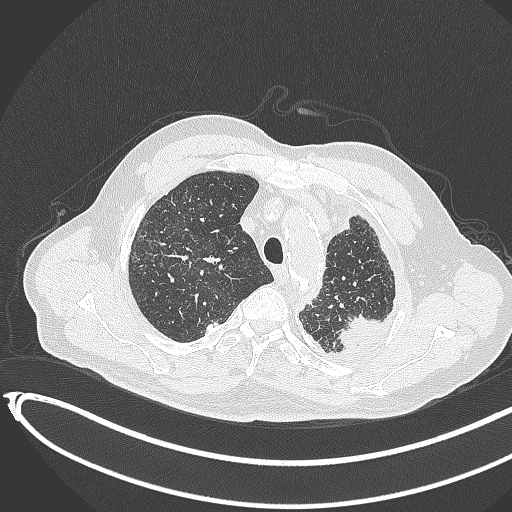
Chest CT, one axial slice; position 347 of 451 along the scan axis; reconstruction kernel B70f; 120 kVp; lung window (W 1500 / L -600 HU); 512 × 512 image matrix. Male patient, age 78 years. From the clinical record (not read from this slice): clinical TNM (as recorded): T1c N0 M1.
Structures marked on this image (rectangle marked by the reading radiologist):
- lung tumour (recorded histology: adenocarcinoma): bounding box [x1, y1, x2, y2] px = [333, 307, 383, 355]